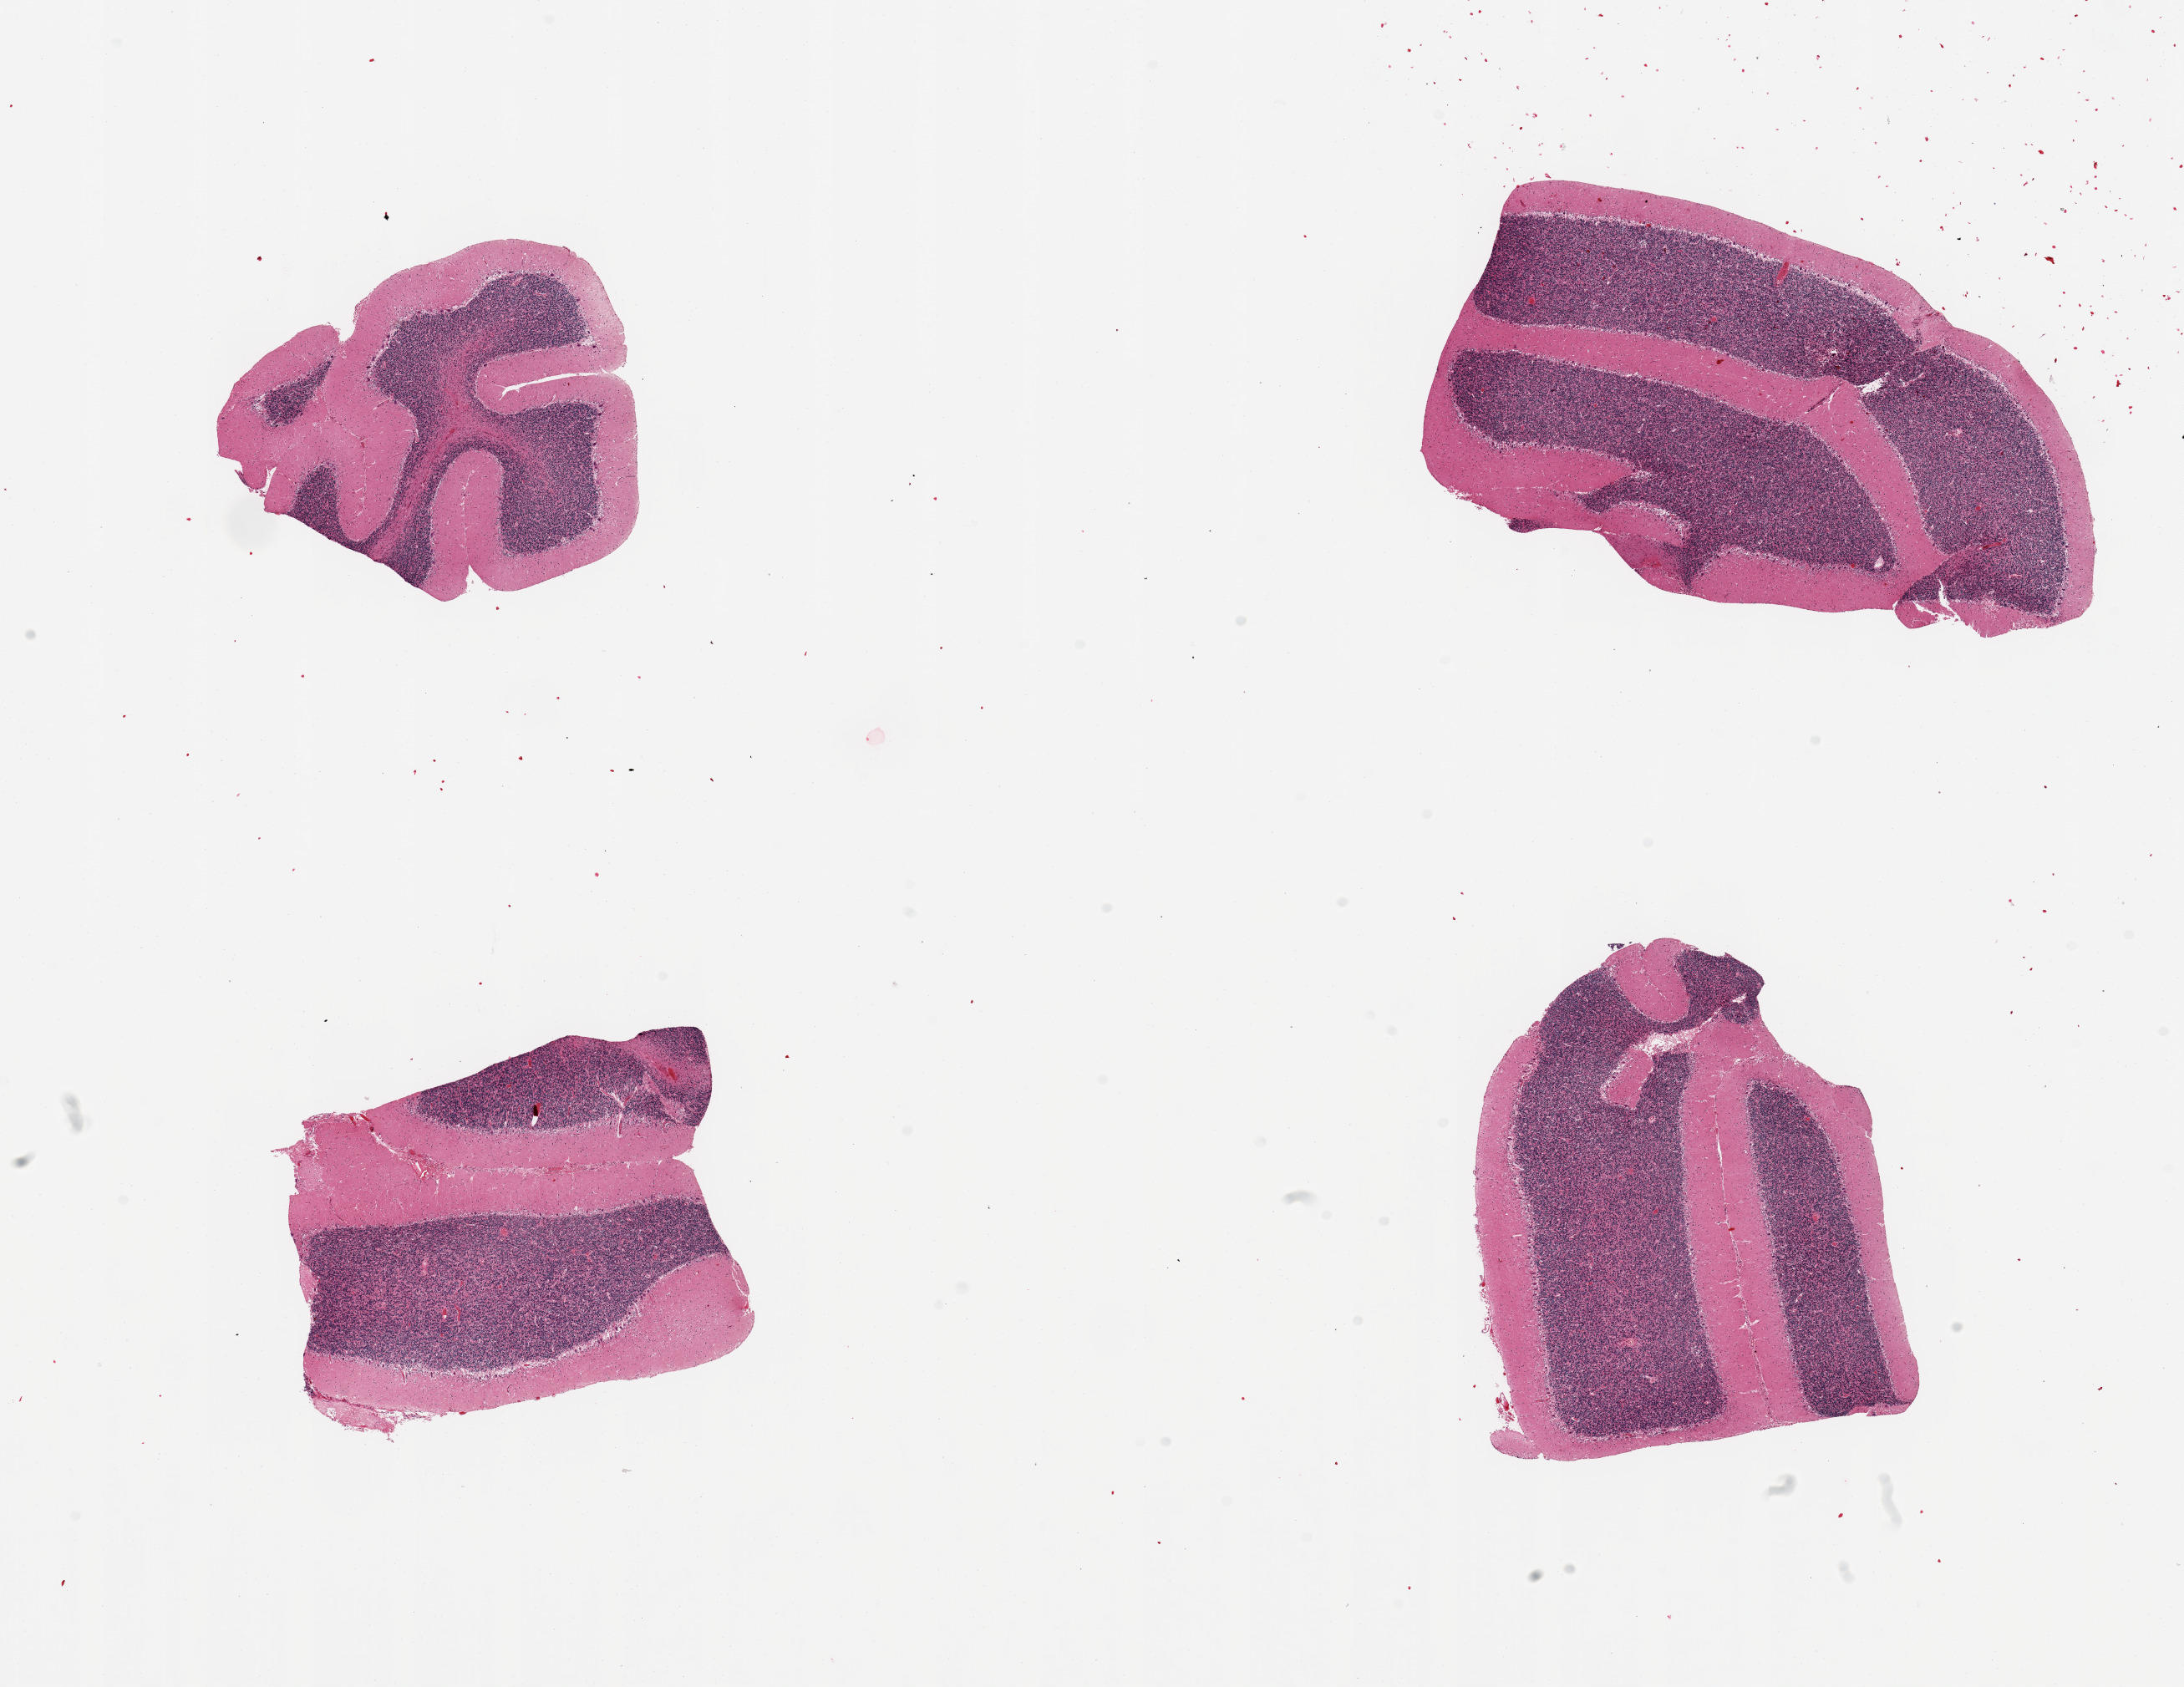
Haematoxylin and eosin whole-slide image — whole scanned area (about 20.7 x 16.0 mm, slide scanned at 20x) shown as a low-resolution overview, PAXgene-fixed, paraffin-embedded tissue, target tissue: cerebellum, donor tissue sample. Male donor.
Reviewer comment on this tissue sample: 4 pieces, no abnormalities.